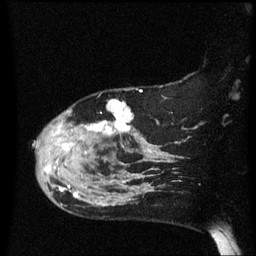
Breast MRI (dynamic contrast-enhanced), one sagittal slice. Slice 48 of 60 in the series (ordered by position). Dynamic contrast-enhanced series, image 2 of 3 at this slice position (ordered by acquisition). 1.5 T. TE 4.2 ms, TR 8.4 ms. 2.2 mm slice thickness. 256 × 256 image matrix. Patient: female, 47 years.
Annotated regions visible in this slice (semi-automatic segmentation, software-assisted and operator-edited):
- analysis volume of interest (the breast-tissue region the enhancement analysis was run in; not a lesion): box from (x=34, y=100) to (x=149, y=206) px
- tumour enhancement mask (voxels above the 70 % enhancement threshold inside the analysis volume of interest): (x=34, y=100)–(x=149, y=202)